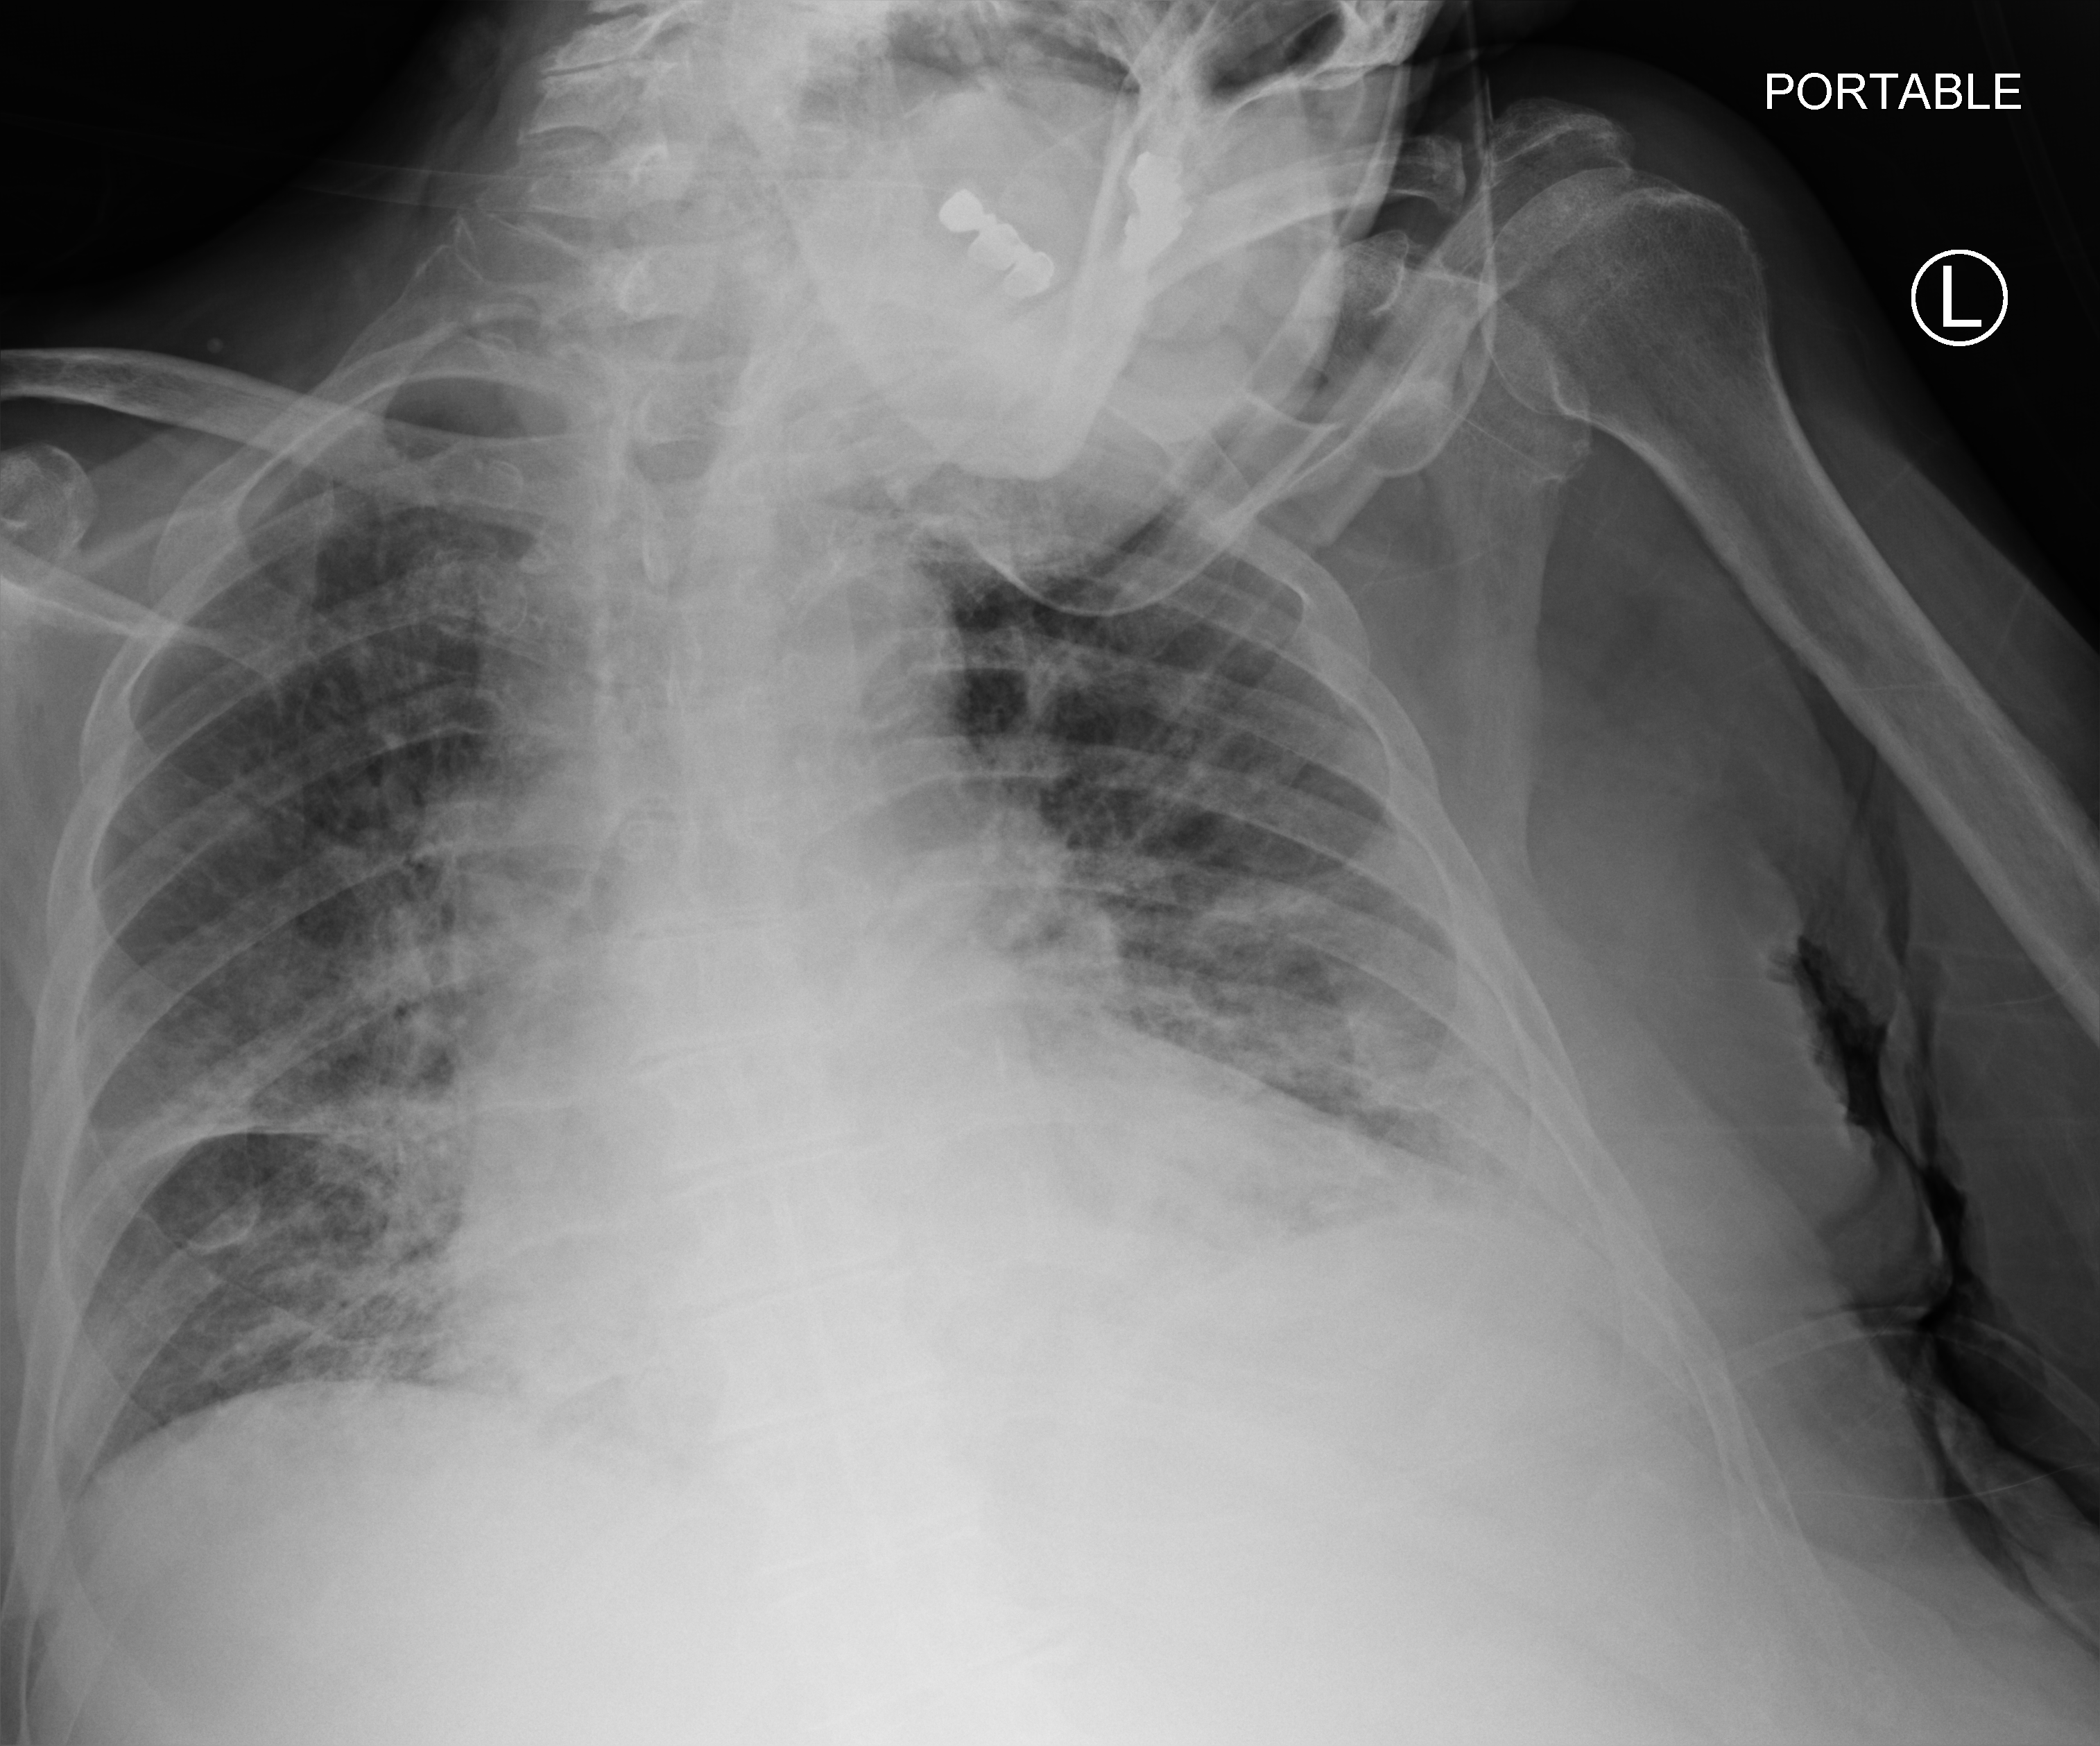
Chest X-ray (portable), anteroposterior (AP) projection. Patient hospitalised with COVID-19; male, aged 75–90 years.
From the hospital-stay record, not from the radiograph (when in the stay this image was taken is not recorded): mechanically ventilated during this hospital stay: no; length of hospital stay: 9 days.